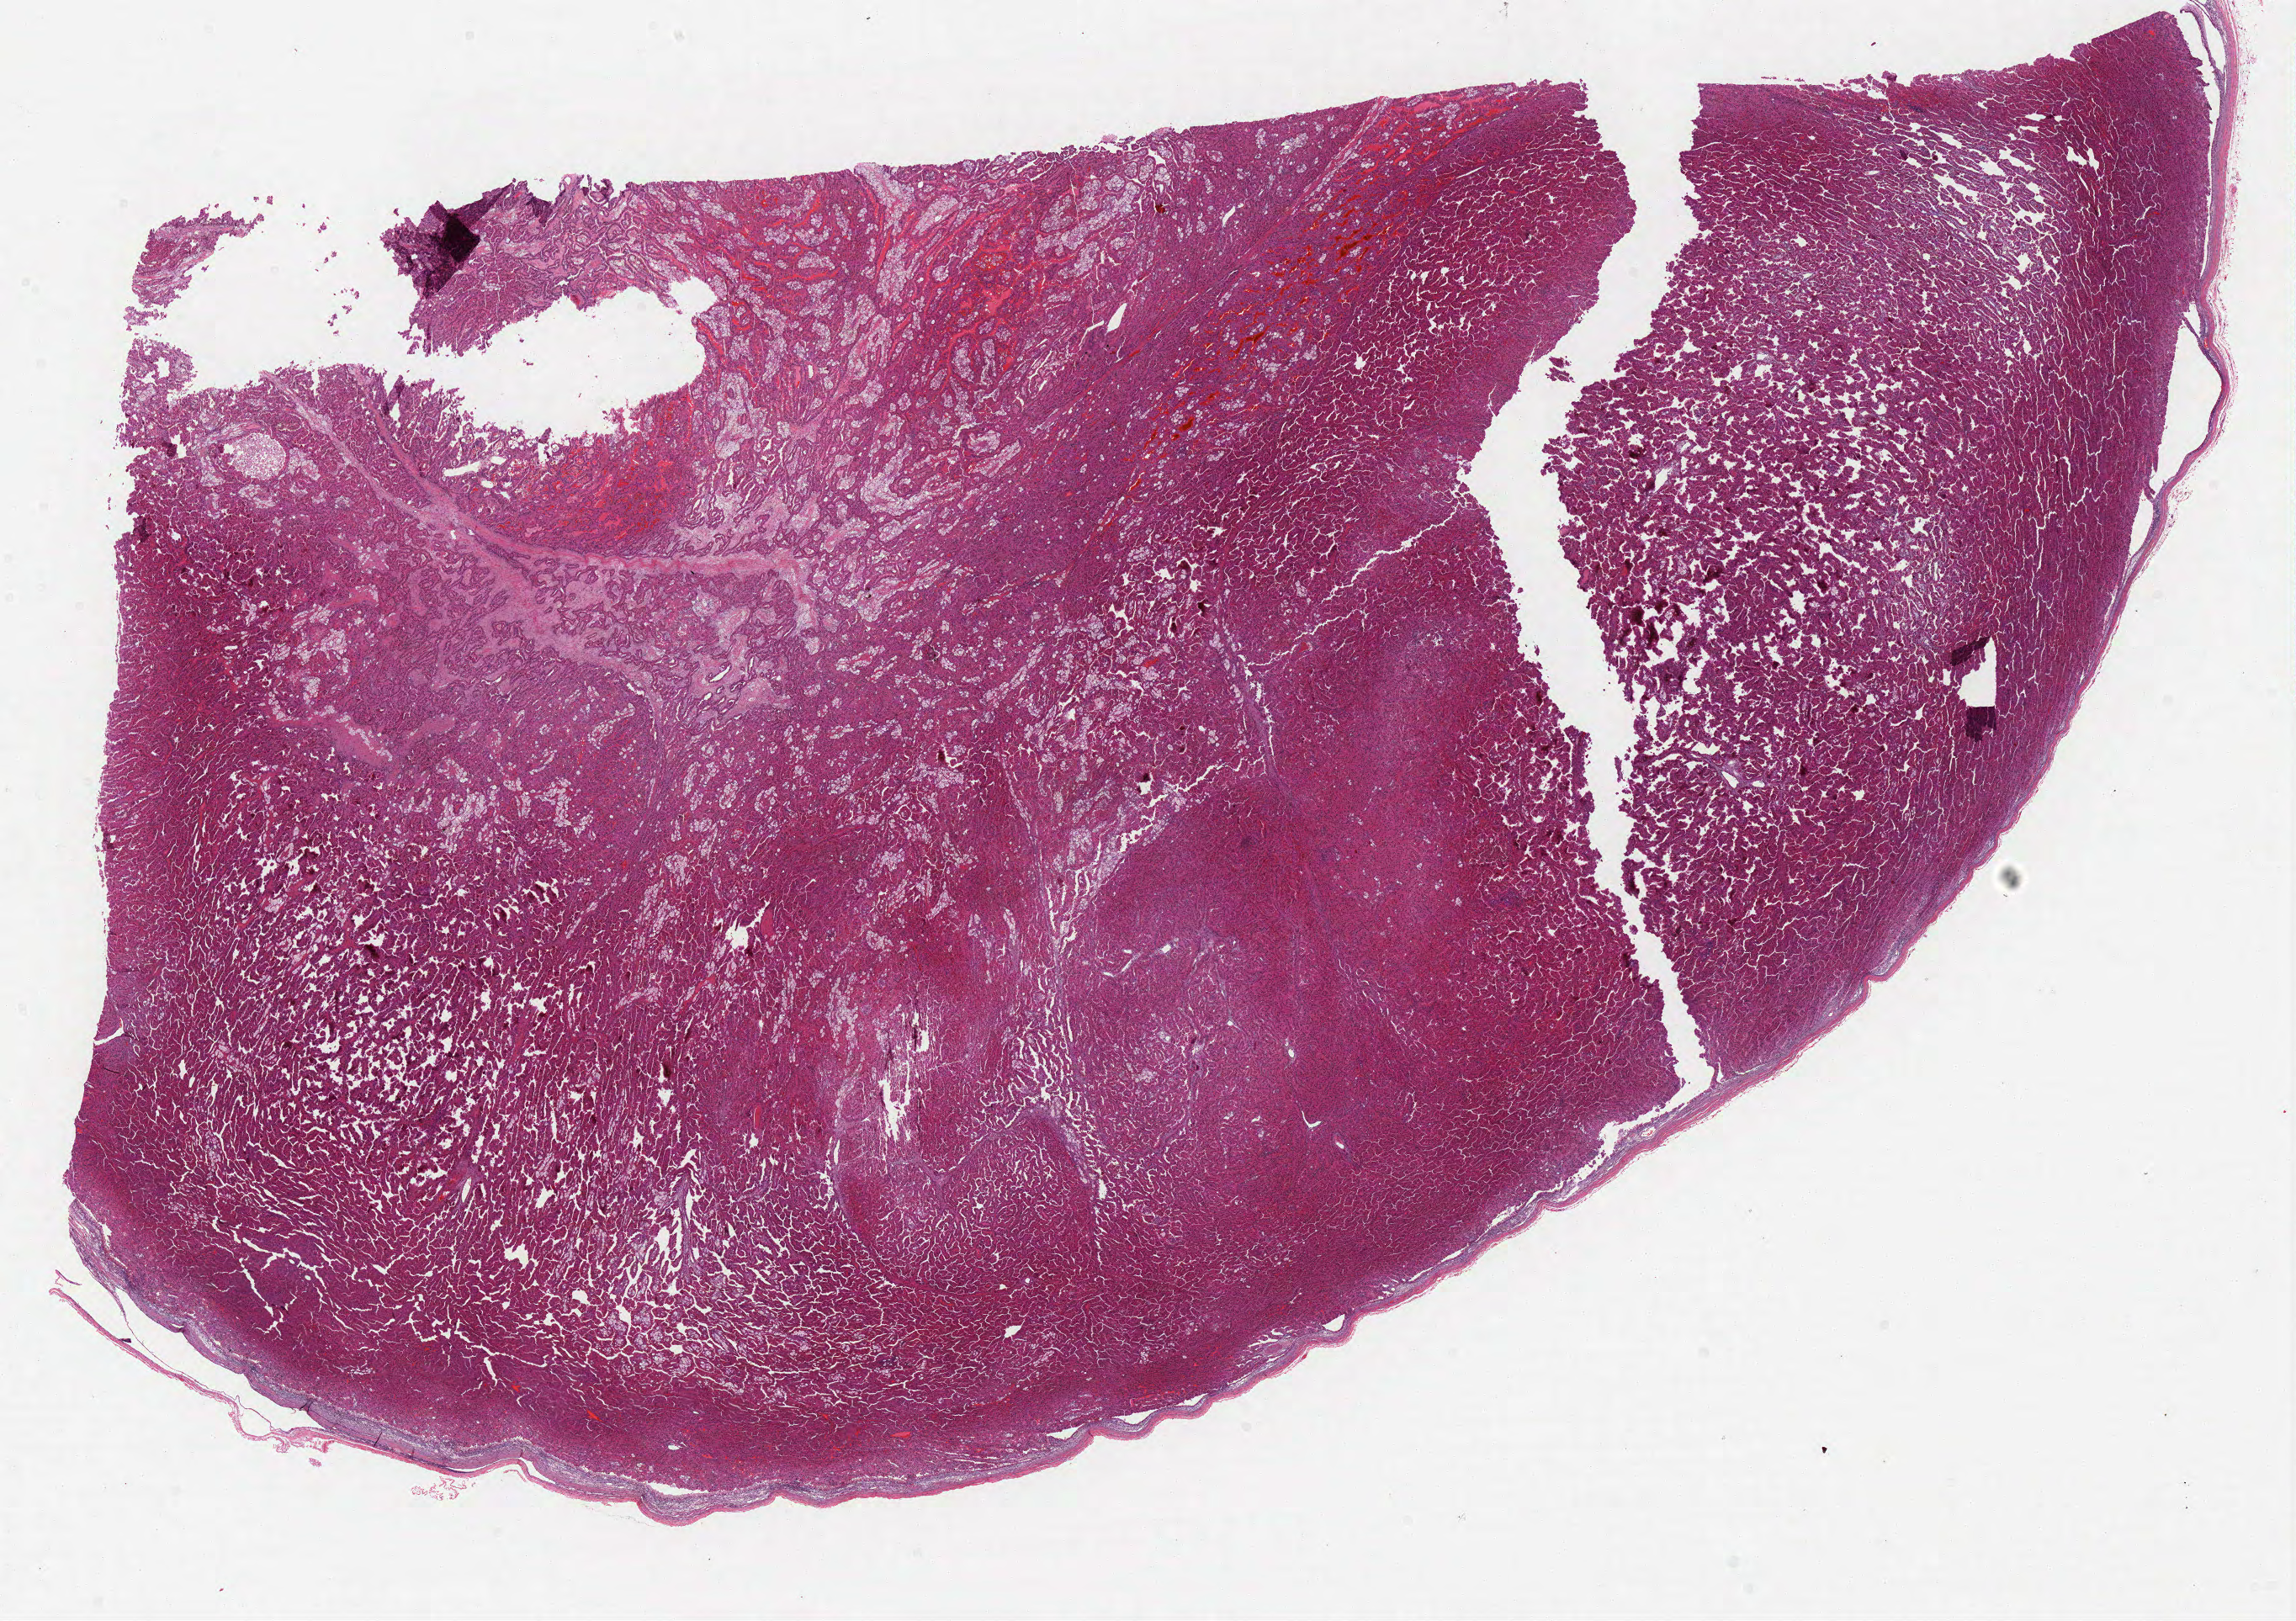
Whole-slide histology image, Hematoxylin and eosin (H&E) stained — whole scanned area (about 21.8 x 15.4 mm, acquisition: 40x scan) shown as a low-resolution overview; FFPE section; kidney, primary tumour sample. Patient: male, age at initial diagnosis 53 years.
Diagnosis: Papillary adenocarcinoma, NOS. TNM: T1a NX M0. AJCC pathologic stage: I (7th edition).